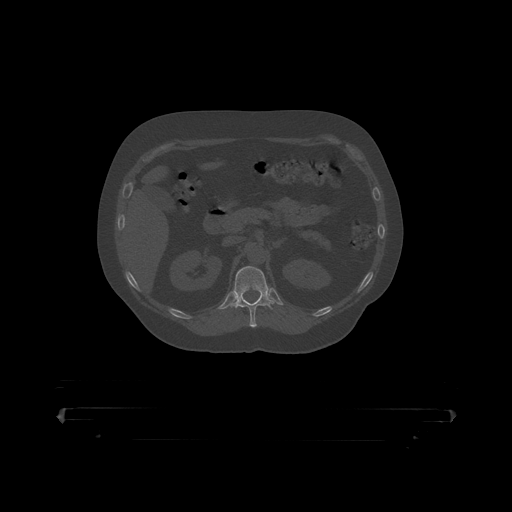
CT including the spine, one axial slice. Position 171 of 390 along the scan axis. Reconstruction kernel STANDARD. Bone window (W 1800 / L 400 HU). 1.25 mm slice thickness. 512 × 512 image matrix, field of view 650 × 650 mm. Male patient, age 60 years. Case-level facts recorded for this patient, not image findings: primary cancer: prostate.
Annotated regions visible in this slice (semi-automatic segmentation, software-assisted and operator-edited):
- T12 vertebra: bounding box <231,267,275,319> (left, top, right, bottom; pixels)